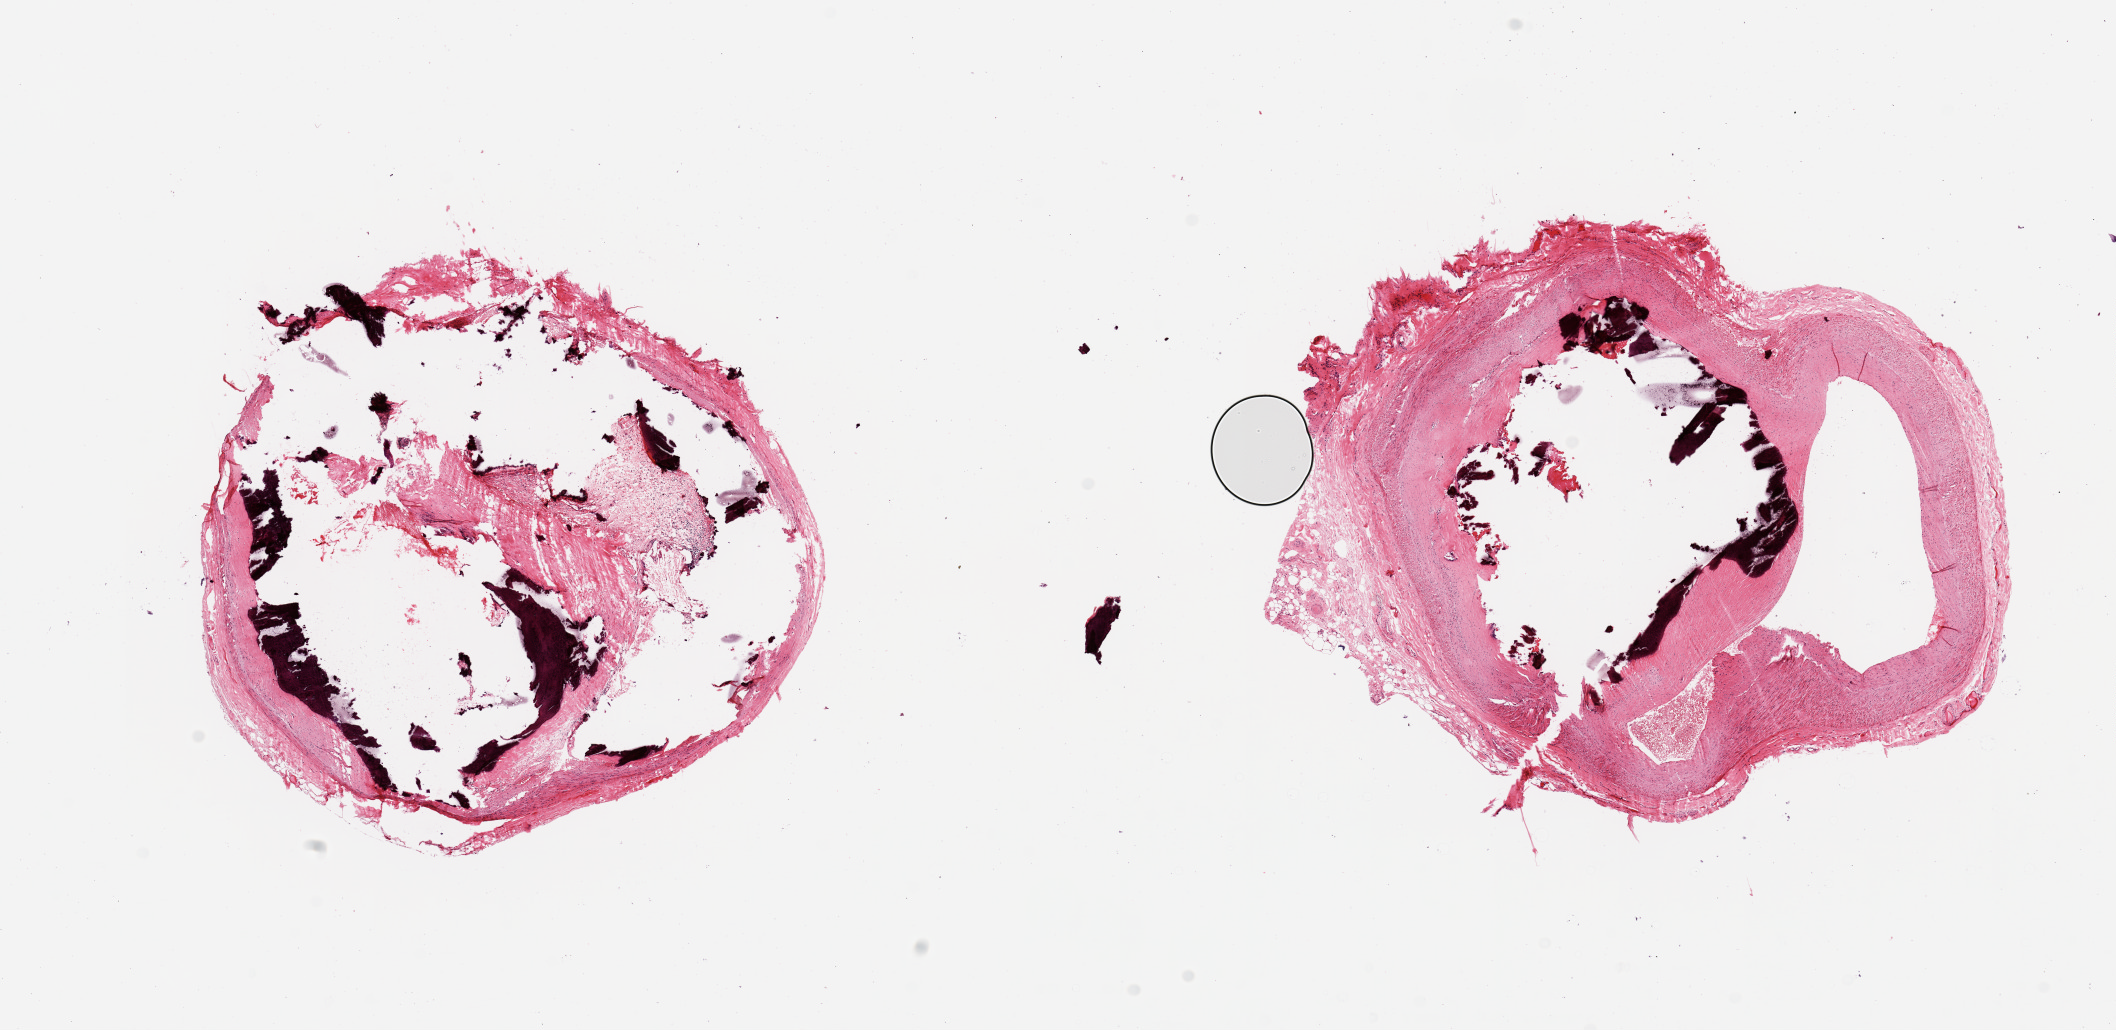
Digitized haematoxylin and eosin-stained section, brightfield — whole scanned area (about 16.7 x 8.1 mm) shown as a low-resolution overview; PAXgene-fixed paraffin-embedded (PFPE) section; section of coronary artery (target tissue); tissue donor sample. Donor sex: male.
Pathologist's review note for this sample: 2 pieces, ~70% occlusive calcifying atherosis; No significant adherant fat.